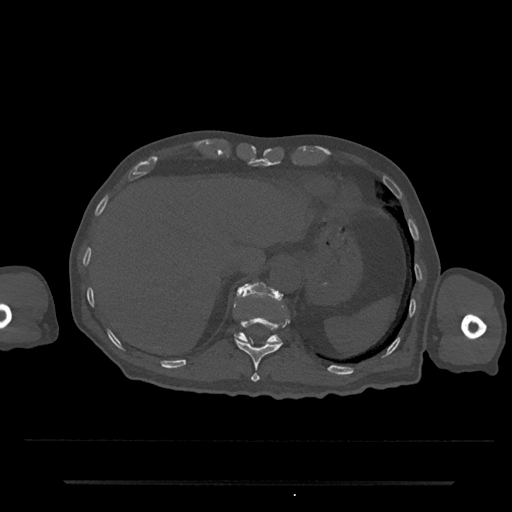
CT including the spine, one axial slice; position 238 of 797 along the scan axis; bone window (W 1800 / L 400 HU); 0.5 mm slice thickness; 512 × 512 image matrix. Patient: male, 74 years. Case-level facts recorded for this patient, not image findings: primary cancer: prostate.
Annotated regions visible in this slice (semi-automatic segmentation, software-assisted and operator-edited):
- T11 vertebra: bounding box [x1, y1, x2, y2] px = [234, 317, 286, 382]
- T12 vertebra: [235, 282, 282, 344]